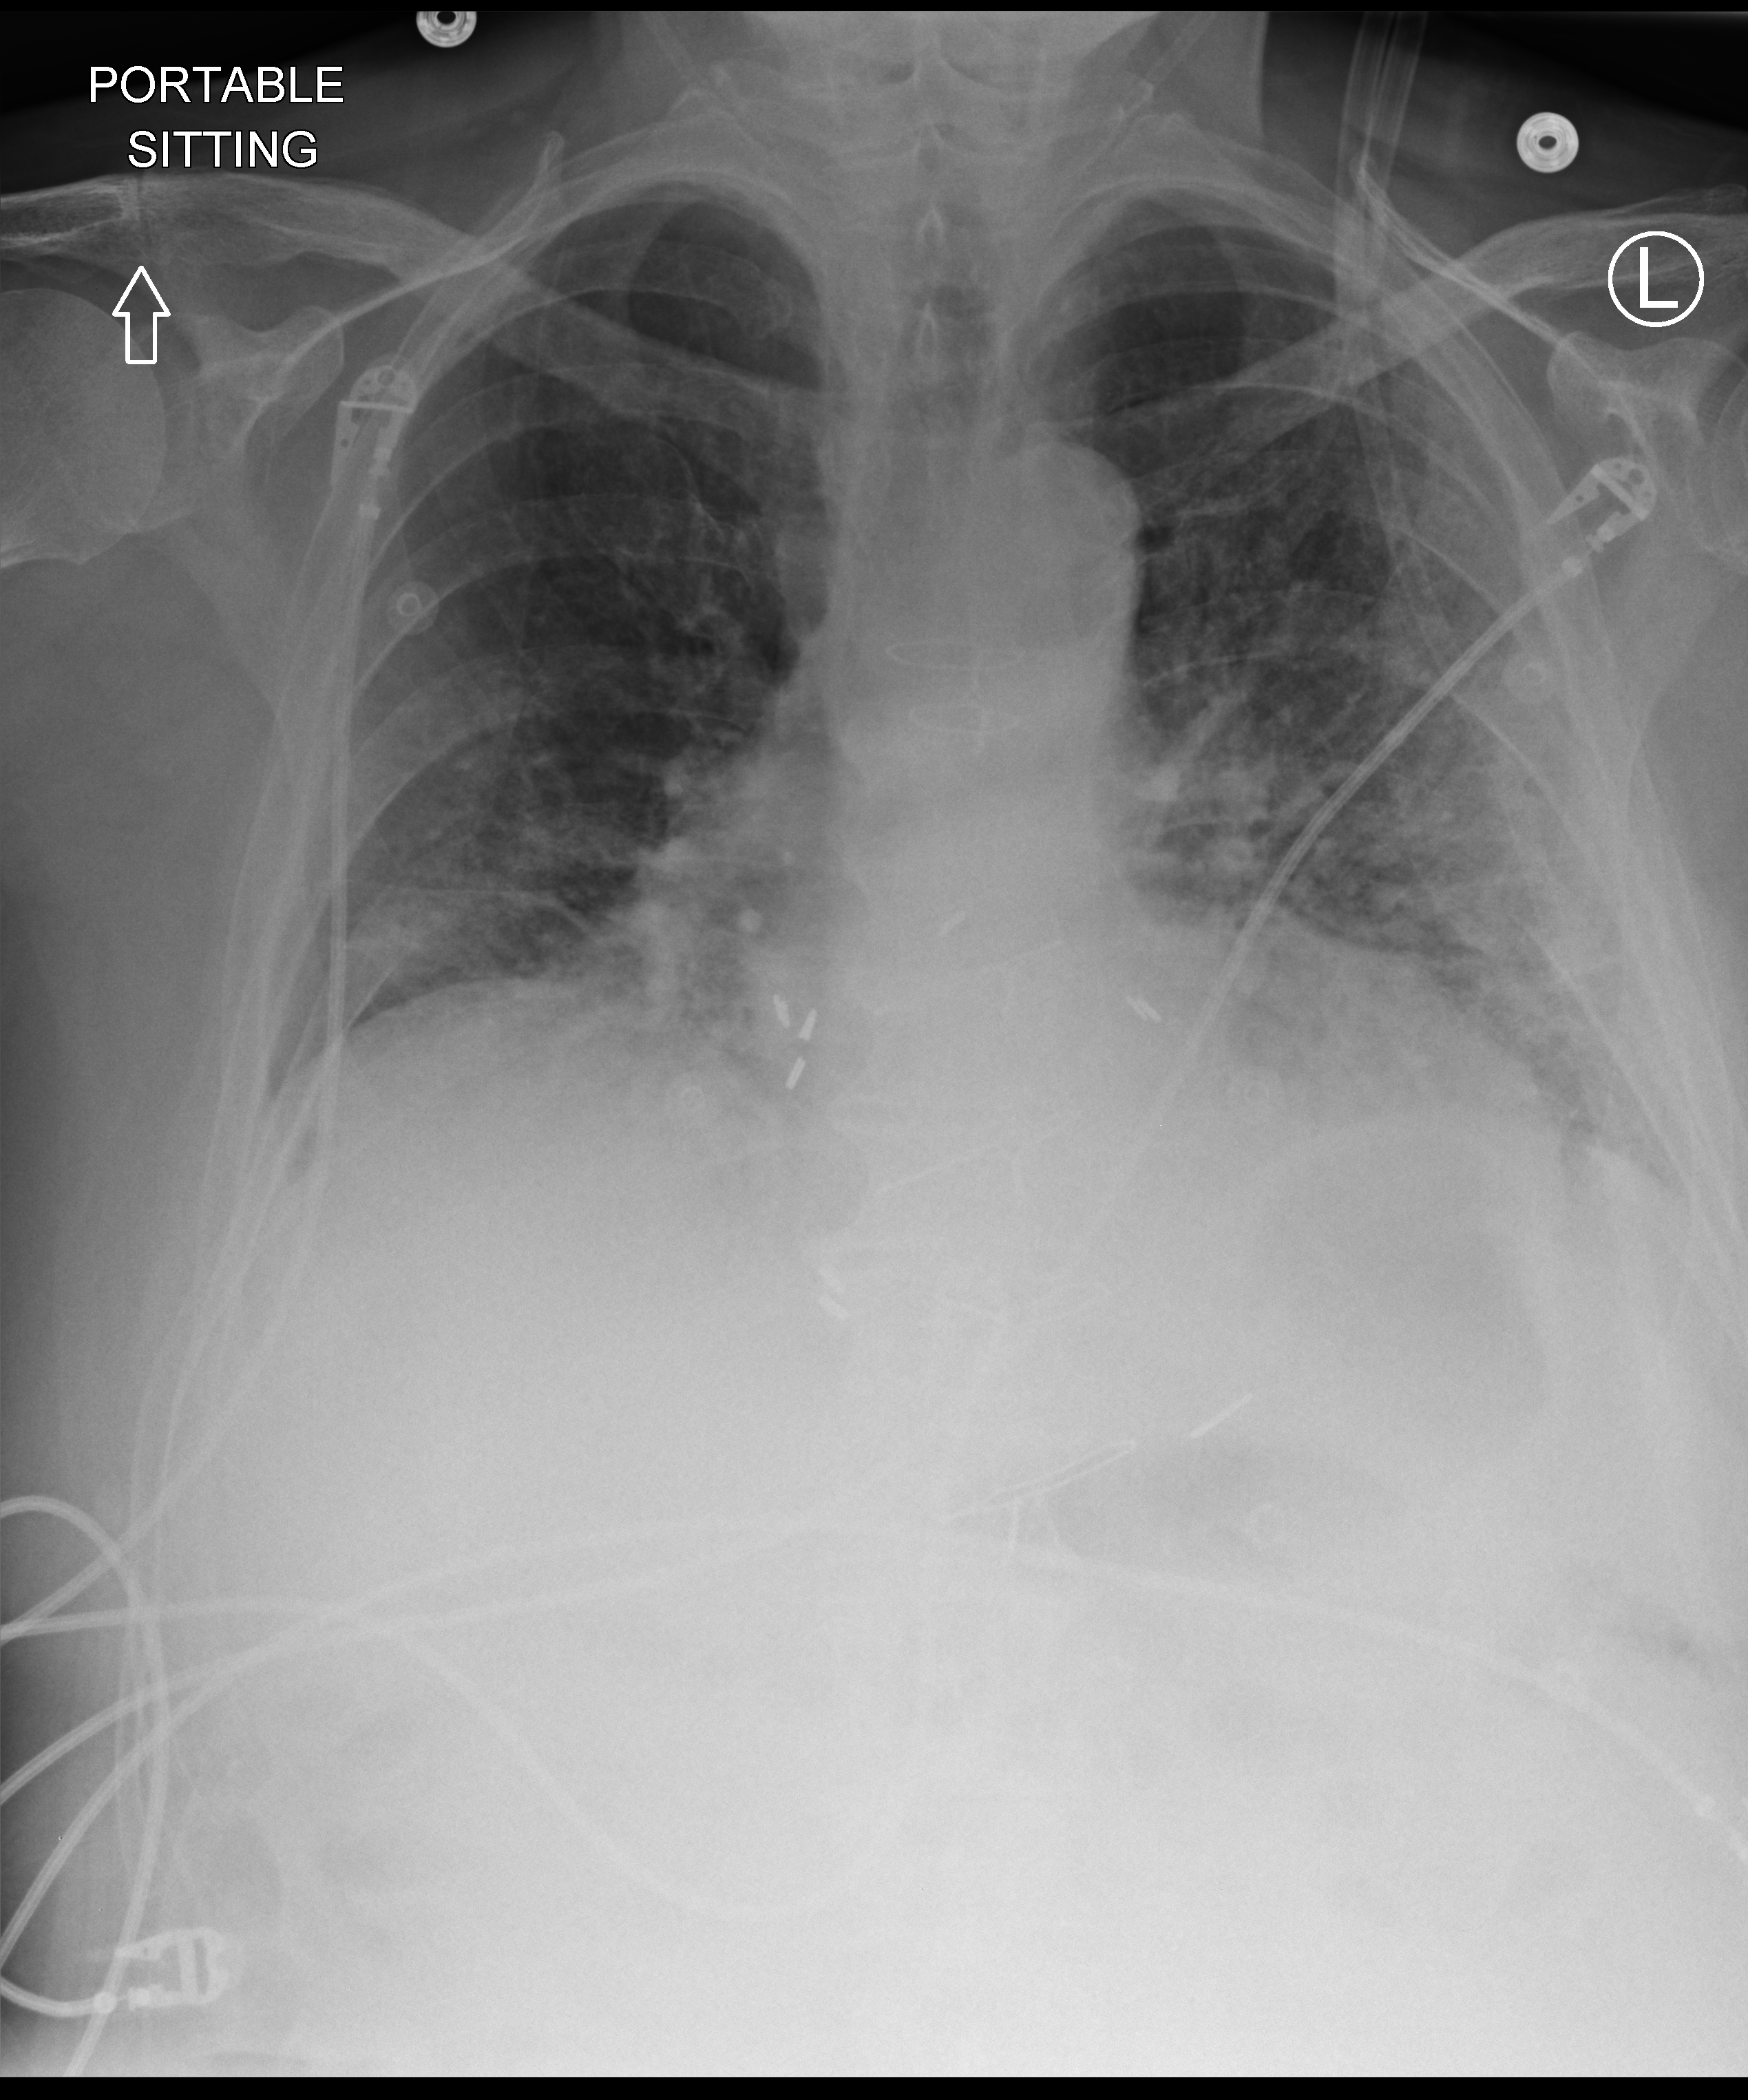
Bedside chest radiograph (computed radiography); anteroposterior (AP) projection. Patient hospitalised with COVID-19; male, aged 75–90 years.
From the hospital-stay record, not from the radiograph (when in the stay this image was taken is not recorded): length of hospital stay: 7 days; hypertension (admission record): yes.